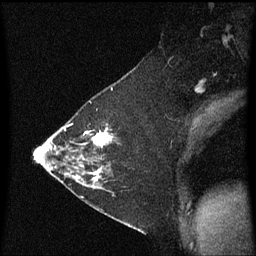
Breast MRI (dynamic contrast-enhanced), one sagittal slice. Position 40 of 60 along the scan axis. Dynamic contrast-enhanced series, image 2 of 3 at this slice position (ordered by acquisition). 1.5 T. TE 4.2 ms, TR 8.4 ms. 2 mm slice thickness. 256 × 256 image matrix, field of view 200 × 200 mm. Female patient, age 36 years. Case-level facts recorded for this patient, not image findings: setting: breast cancer imaged before/during neoadjuvant chemotherapy; receptor status: HR-positive, HER2-negative.
Structures marked on this image (semi-automatic segmentation, software-assisted and operator-edited):
- analysis volume of interest (the breast-tissue region the enhancement analysis was run in; not a lesion): bounding box <72,116,119,187> (left, top, right, bottom; pixels)
- tumour enhancement mask (voxels above the 70 % enhancement threshold inside the analysis volume of interest): <76,128,113,183>